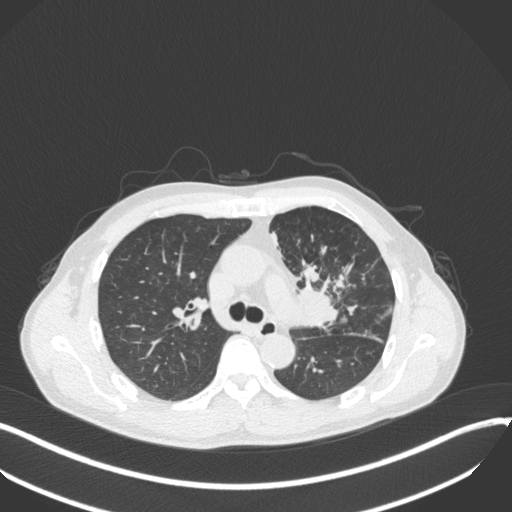
Chest CT, one axial slice. Slice 223 of 411 in the series (ordered by position). Reconstruction kernel B31f. Lung window (W 1500 / L -600 HU). 1 mm slice thickness. 512 × 512 image matrix, field of view 400 × 400 mm. Male patient, age 56 years. Case-level facts recorded for this patient, not image findings: clinical TNM (as recorded): T2a N0 M0.
Outlined on this slice (rectangle marked by the reading radiologist):
- lung tumour (recorded histology: squamous cell carcinoma): bounding box [x1, y1, x2, y2] px = [296, 260, 345, 332]